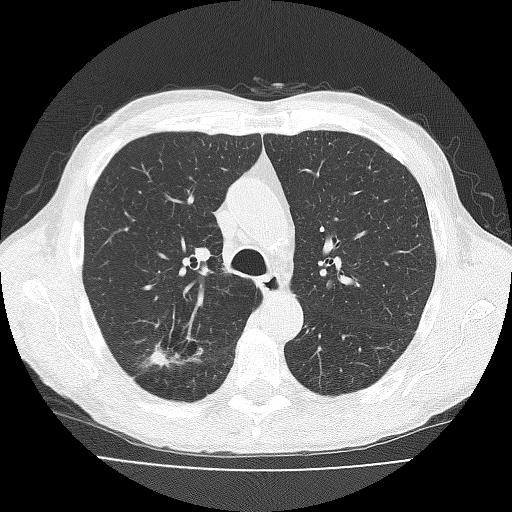
Axial slice from a low-dose chest CT screening exam; third screening round (two years after baseline); lung window (W 1500 / L -600 HU); 2 mm slice thickness; lung (sharp) reconstruction kernel (FC51); slice 61 of 181 in the series. Male participant, aged 73 years at enrolment. Current smoker at enrolment.
• Expert-annotated lung lesion, box from (x=140, y=326) to (x=192, y=378) px.
• Screening reader's record for this exam (one nodule recorded; not confirmed to be the boxed lesion): non-calcified nodule or mass ≥4 mm, right upper lobe, 11 × 10 mm, spiculated (stellate) margins, soft tissue attenuation, pre-existing on the prior screen: no.
• Participant outcome: lung cancer diagnosed 38 days after this screen — adenosquamous carcinoma, right upper lobe, well differentiated (G1), stage IA (AJCC 6th edition), 20 mm at pathology.